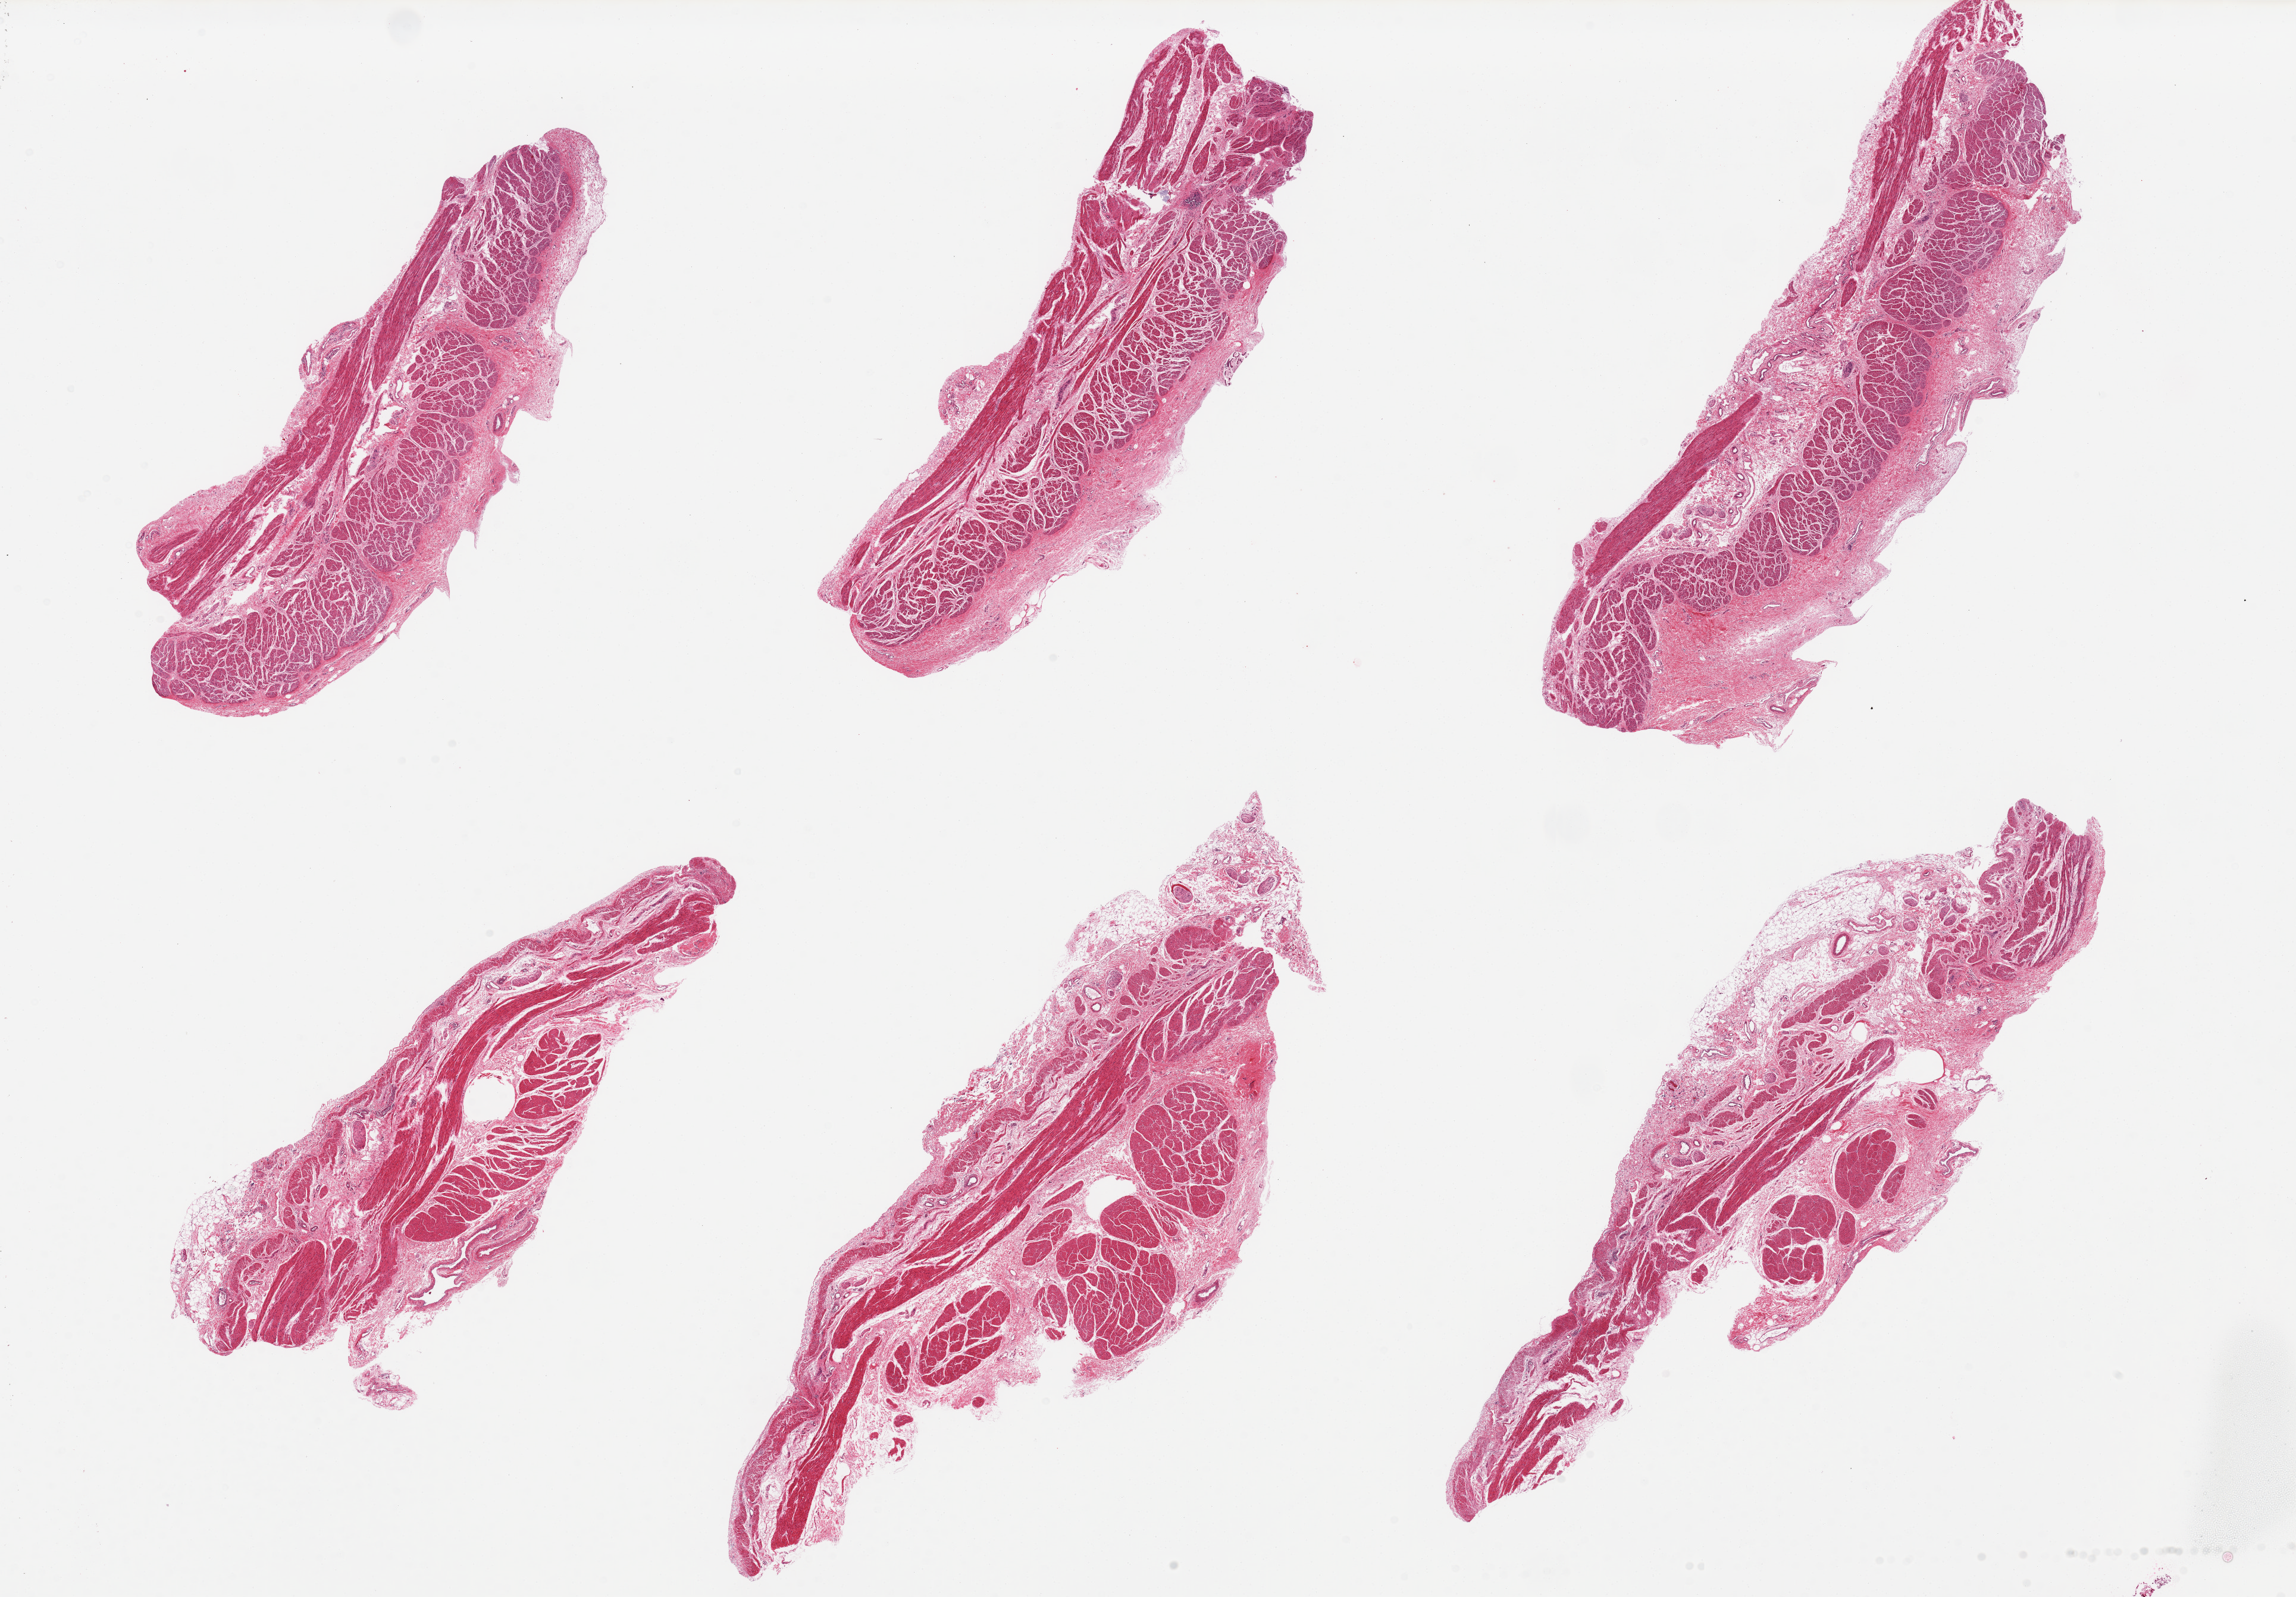
Haematoxylin and eosin whole-slide image — a low-resolution overview of the entire scanned area, about 30.5 x 21.2 mm (from a 20x scan). PAXgene-fixed, paraffin-embedded tissue. Section of gastroesophageal junction (target tissue). Donor tissue sample. Donor: female.
• reviewer comment on this tissue sample: 6 pieces, all muscularis